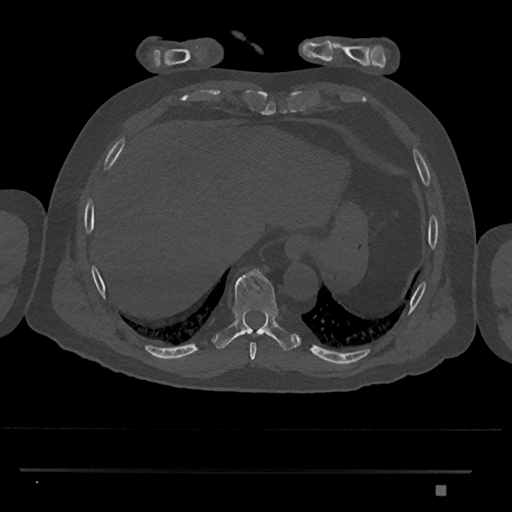
CT including the spine, one axial slice. Slice 1067 of 1134 in the series (ordered by position). Bone window (W 1800 / L 400 HU). 0.5 mm slice thickness. 512 × 512 image matrix. Male patient, age 65 years. Case-level facts recorded for this patient, not image findings: primary cancer: prostate.
Annotated regions visible in this slice (semi-automatically segmented with operator editing):
- T8 vertebra: box from (x=250, y=343) to (x=257, y=360) px
- T9 vertebra: (x=215, y=269)–(x=297, y=351)